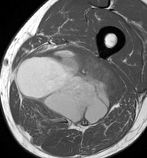
MRI of an extremity soft-tissue mass, one axial slice. MR volume resampled by the dataset authors to the PET/CT grid (not the native acquisition matrix). 3.27 mm slice thickness. 147 × 158 image matrix. Male patient. Case-level facts recorded for this patient, not image findings: histological type: undifferentiated pleomorphic liposarcoma; grade: high; site of the primary tumour: left thigh.
Structures marked on this image (expert contour drawn on MRI and transferred to this co-registered scan by the dataset authors):
- gross tumour volume including surrounding oedema: bounding box [x1, y1, x2, y2] px = [16, 47, 120, 130]
- gross tumour volume (mass): [16, 47, 120, 128]